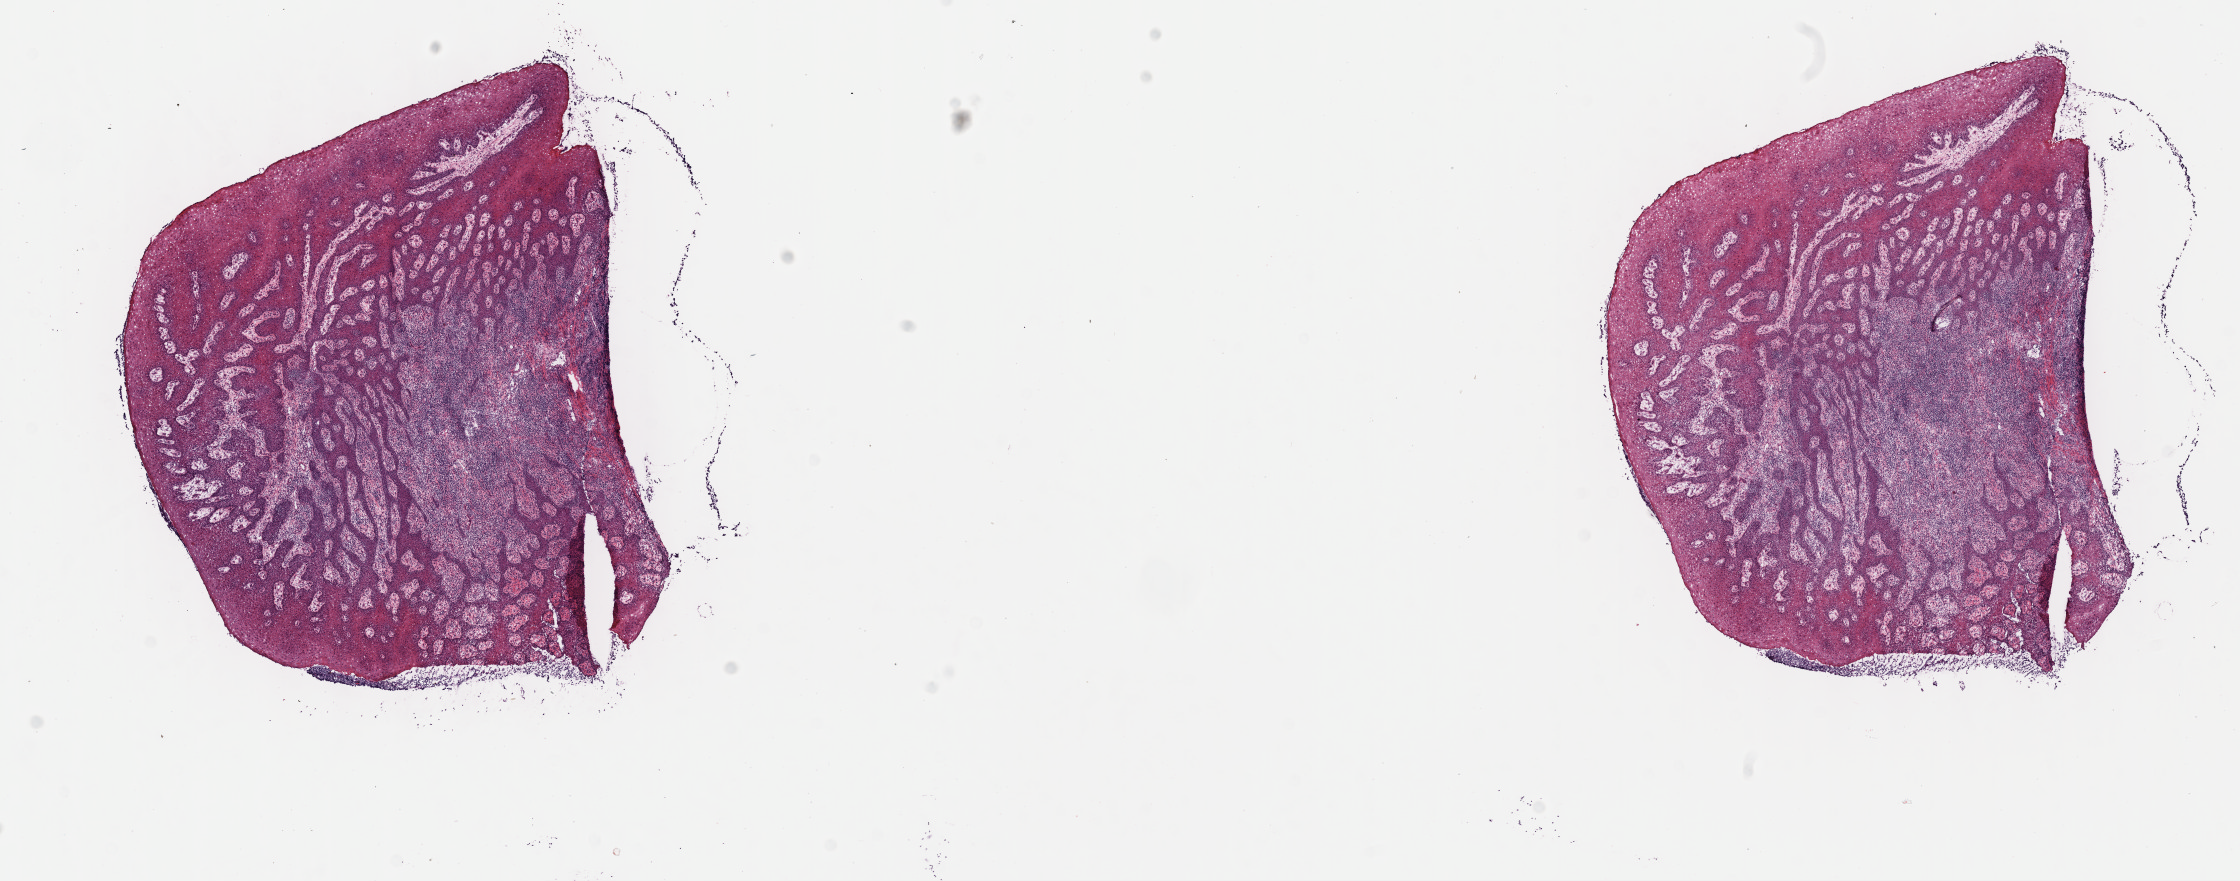
H&E whole-slide image — low-resolution overview of the scanned area, about 18.1 x 7.1 mm; frozen section (tissue freezing medium); primary tumor; anatomic site: mandible. Male, age 5 years at initial diagnosis. Slide review estimates, as recorded: tumor cells 90%, tumor nuclei 90%, stromal cells 10%, necrosis 0%, normal cells 0%. Inflammatory infiltration, as recorded: lymphocyte infiltration 5%, monocyte infiltration 5%, neutrophil infiltration 0%.
• Ann Arbor stage (patient): Stage I
• histologic diagnosis: Burkitt lymphoma, NOS